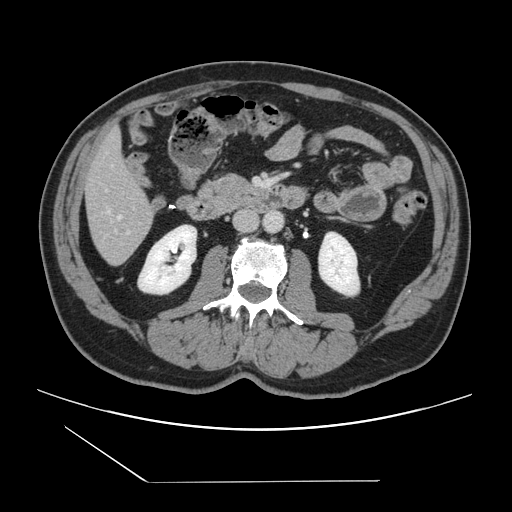
Contrast-enhanced abdominal CT, one axial slice. Position 40 of 157 along the scan axis. Intravenous contrast given. Soft-tissue window (W 400 / L 40 HU). 2.5 mm slice thickness. 512 × 512 image matrix, field of view 407 × 407 mm. Male patient, age 61 years. Case-level facts recorded for this patient, not image findings: diagnosis: colorectal cancer liver metastases, imaged before liver resection; multiple liver metastases: yes; largest metastasis: 5.5 cm.
Structures marked on this image (expert manual segmentation):
- hepatic veins: bounding box <109,211,121,219> (left, top, right, bottom; pixels)
- liver: <85,131,155,264>
- planned liver remnant (the part of the liver to remain after resection): <85,132,150,218>
- portal vein (with intrahepatic branches): <128,231,130,233>